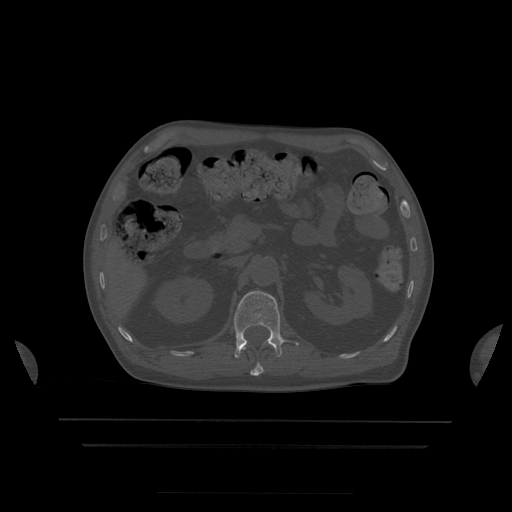
CT including the spine, one axial slice. Position 178 of 522 along the scan axis. Bone window (W 1800 / L 400 HU). 1.25 mm slice thickness. 512 × 512 image matrix, field of view 436 × 436 mm. Patient age 68 years. Case-level facts recorded for this patient, not image findings: primary cancer: urothelial.
Outlined on this slice (semi-automatic segmentation, software-assisted and operator-edited):
- L1 vertebra: box from (x=234, y=291) to (x=299, y=358) px
- T12 vertebra: (x=244, y=348)–(x=264, y=376)